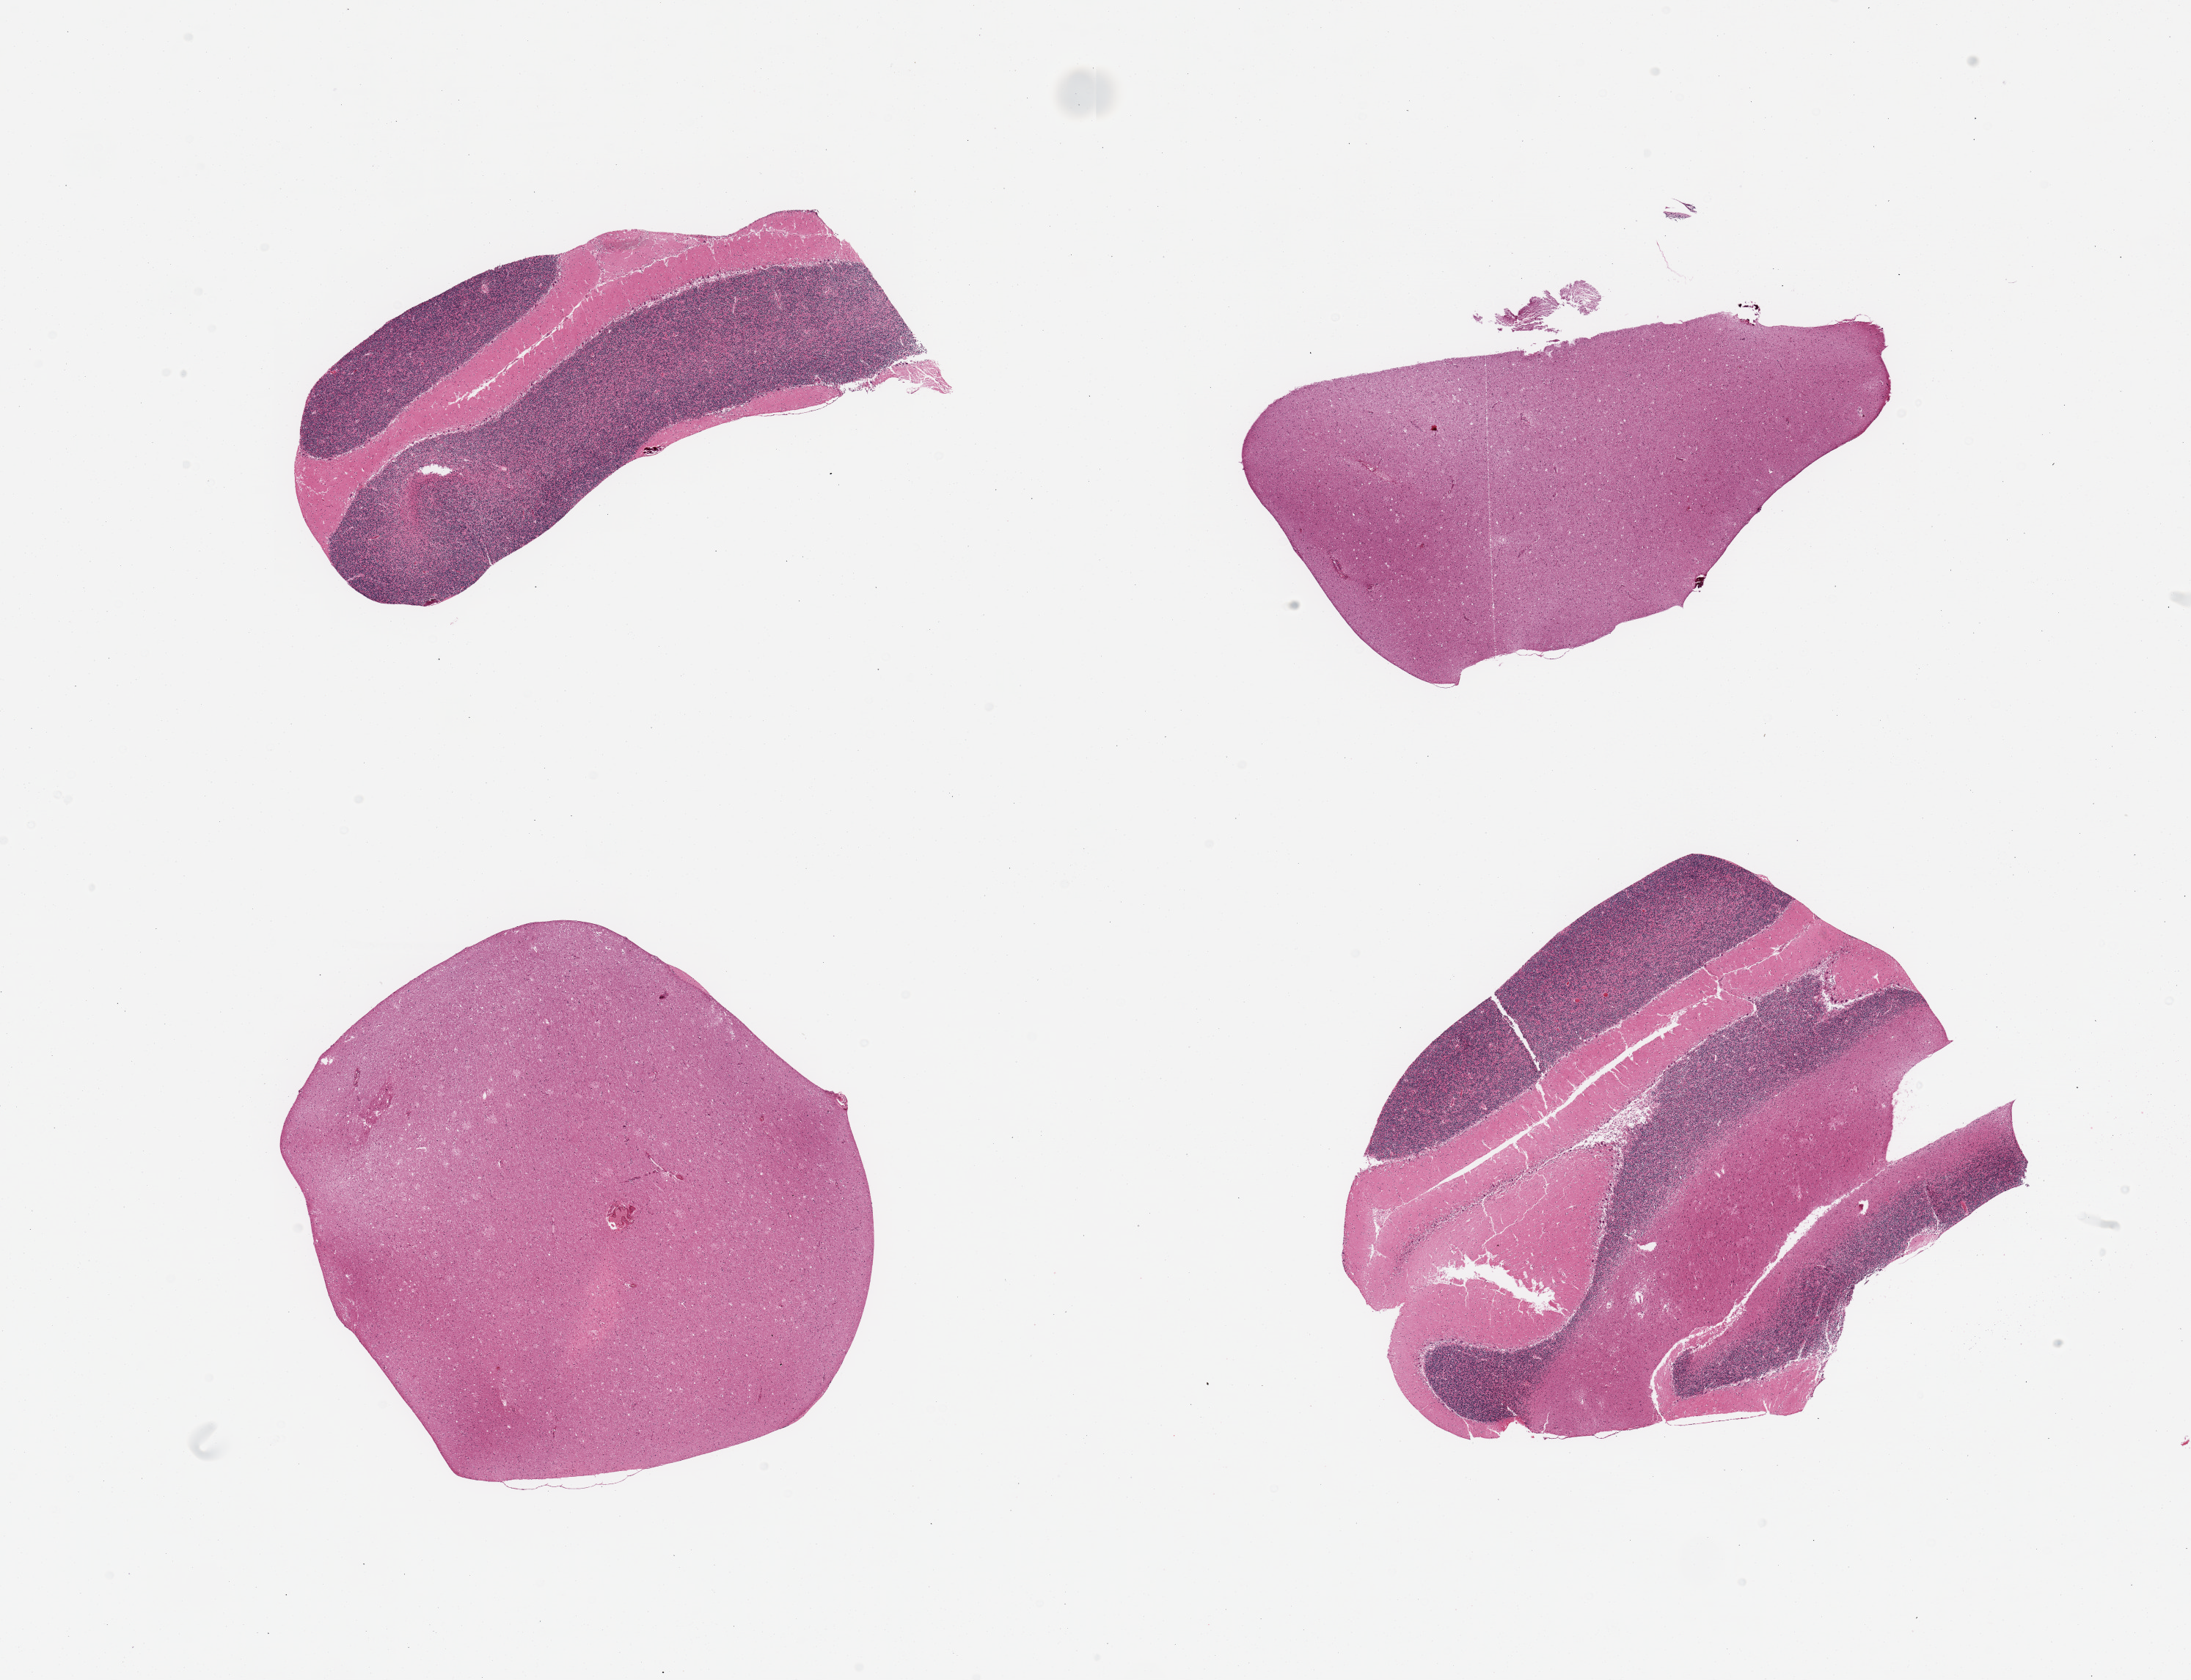
Digitized H&E-stained section, low-resolution overview of the scanned area, about 23.6 x 18.1 mm (slide scanned at 20x). PAXgene-fixed, paraffin-embedded tissue. Sampled site (target tissue): cerebellum. Tissue donor sample. Male donor.
Review note (as recorded): 2 pieces cerebellum, 2 pieces cortex.